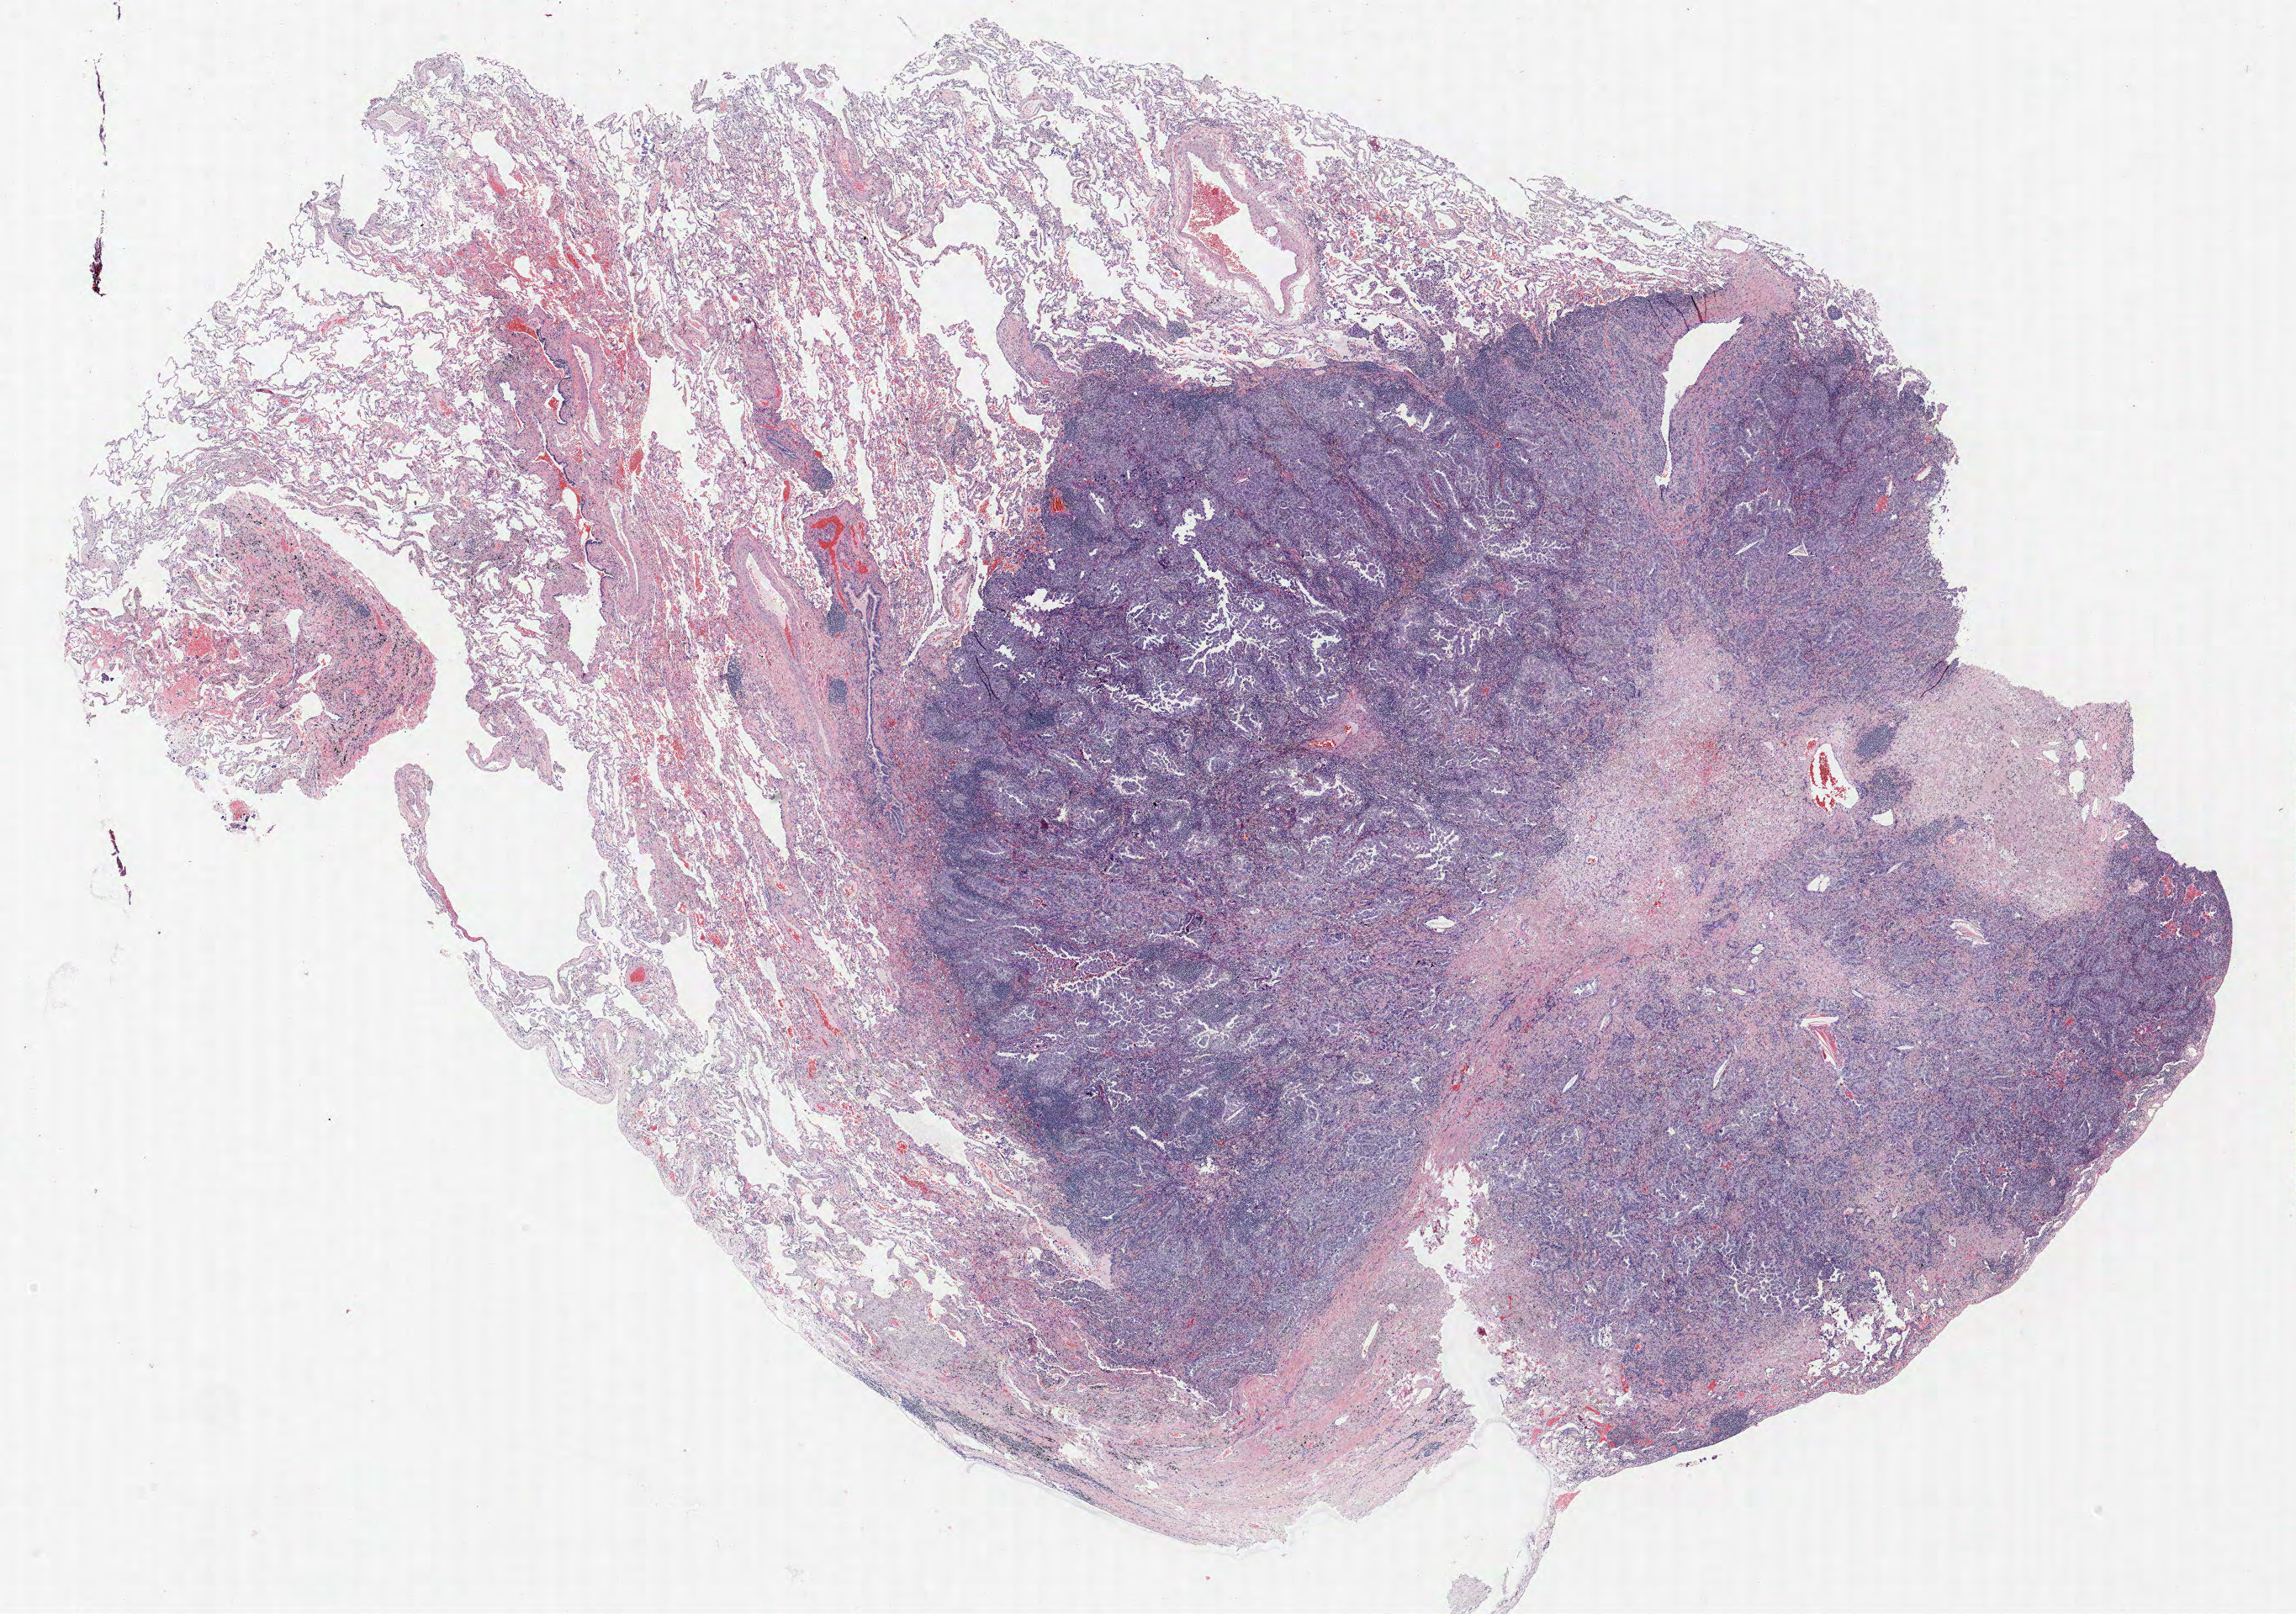
Whole-slide histology image, H&E-stained, shown as a low-resolution overview of the whole scanned area (about 21.8 x 15.4 mm, from a 40x scan). Formalin-fixed paraffin-embedded (FFPE) section. Lung. Male, age 63 at enrolment. Grade: moderately differentiated (G2).
* participant's lung-cancer diagnosis: Adenocarcinoma, NOS
* primary tumour location (clinical record): left upper lobe
* tumour size (pathology): 14 mm
* stage (AJCC 6th edition): IB